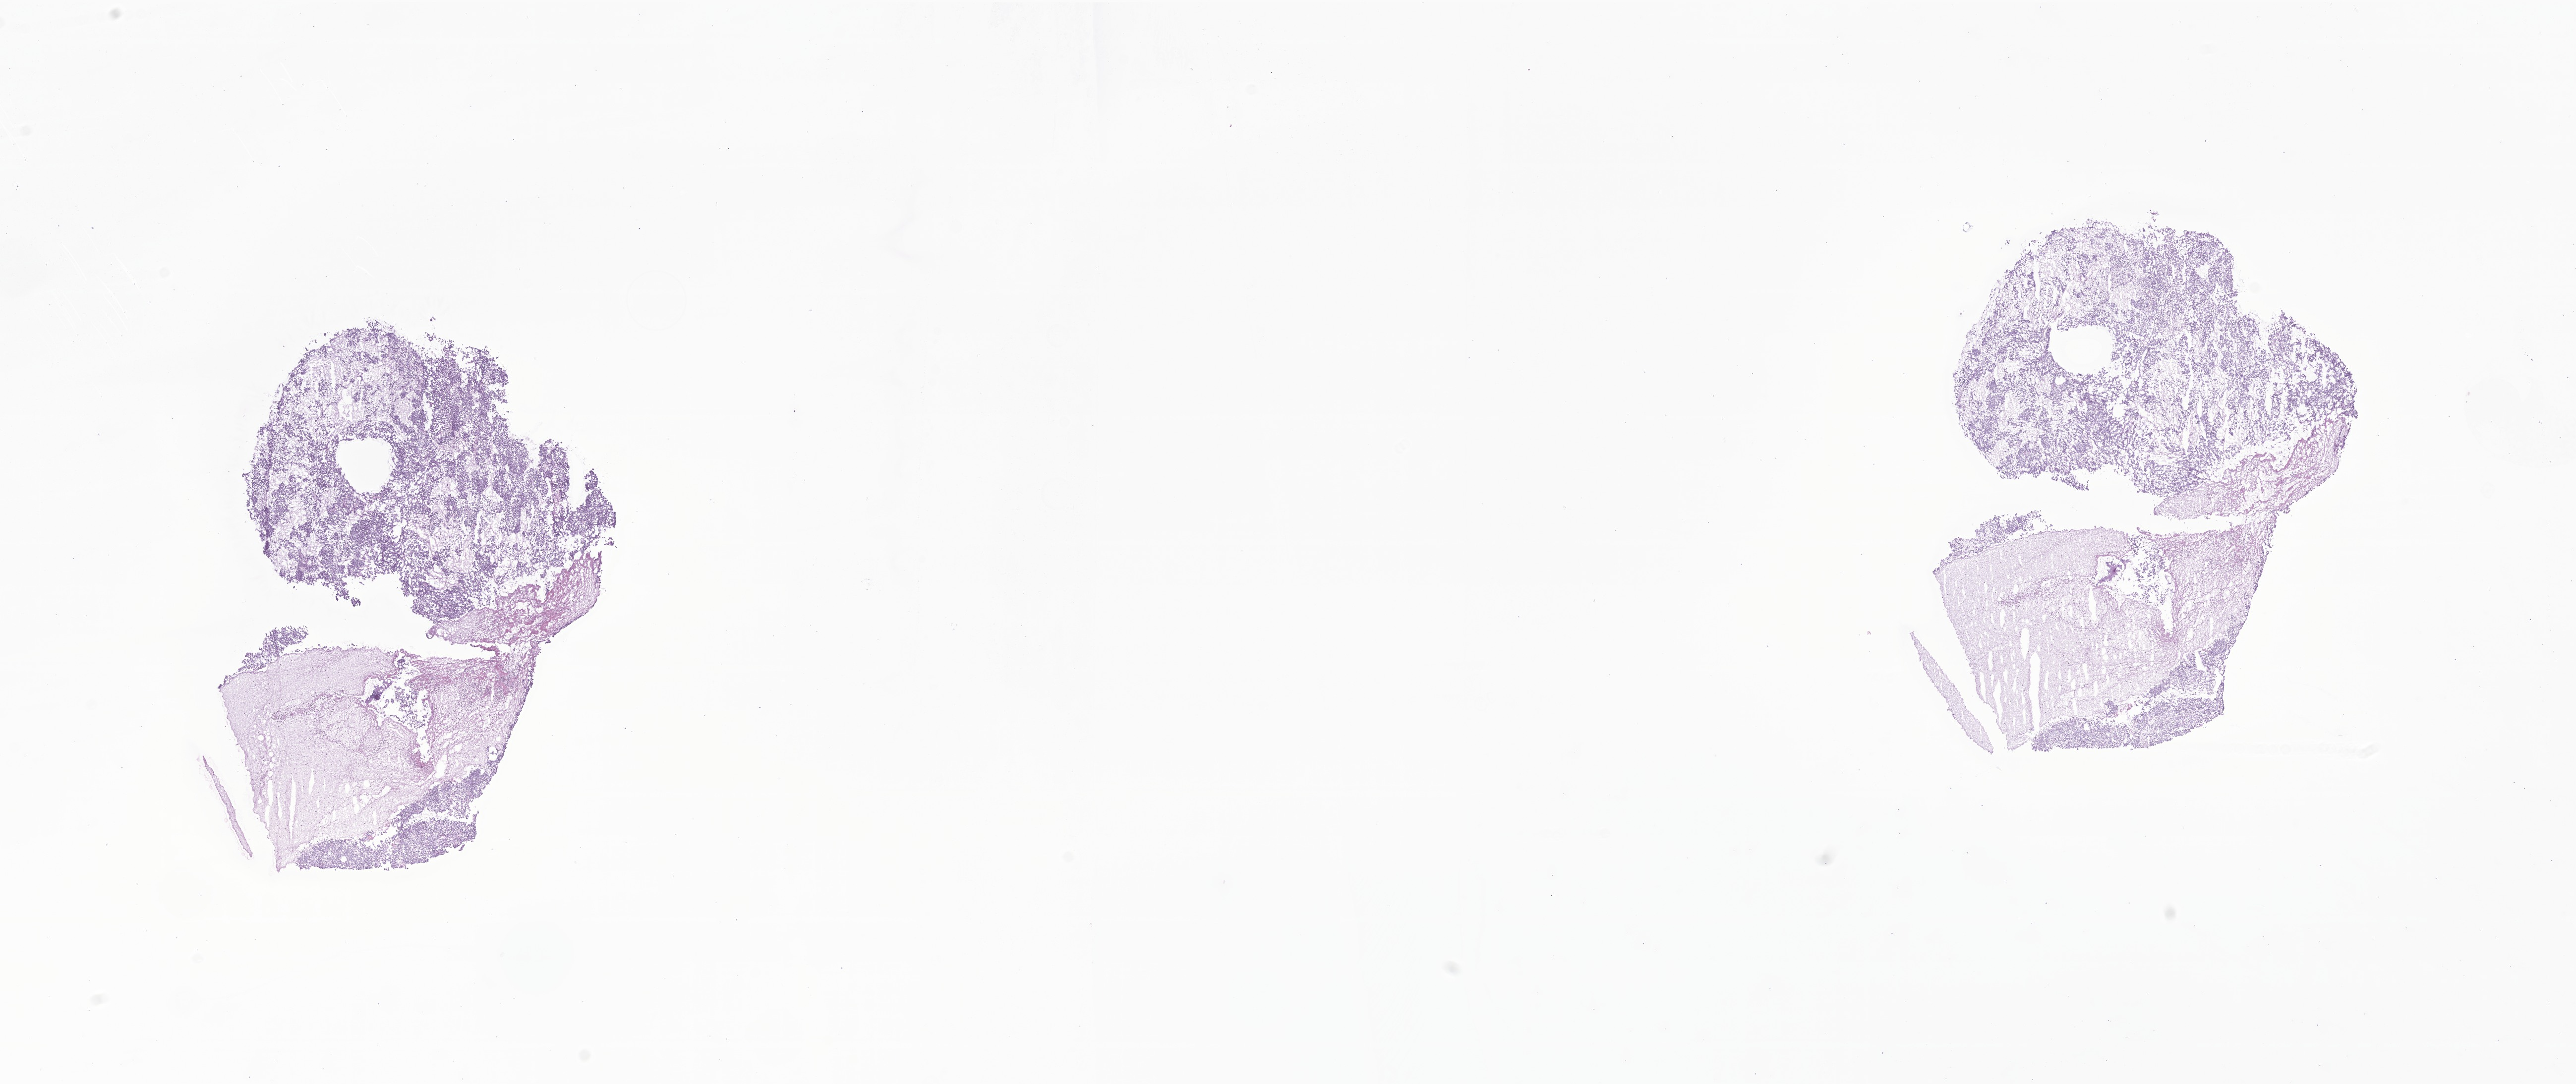
Digitized haematoxylin and eosin-stained section of tumor tissue from the cerebellum — shown as a low-resolution overview of the whole scanned area (about 21.9 x 9.2 mm); frozen section. Male patient, age 154 months (12 years 10 months).
- recorded diagnosis: Medulloblastoma, NOS